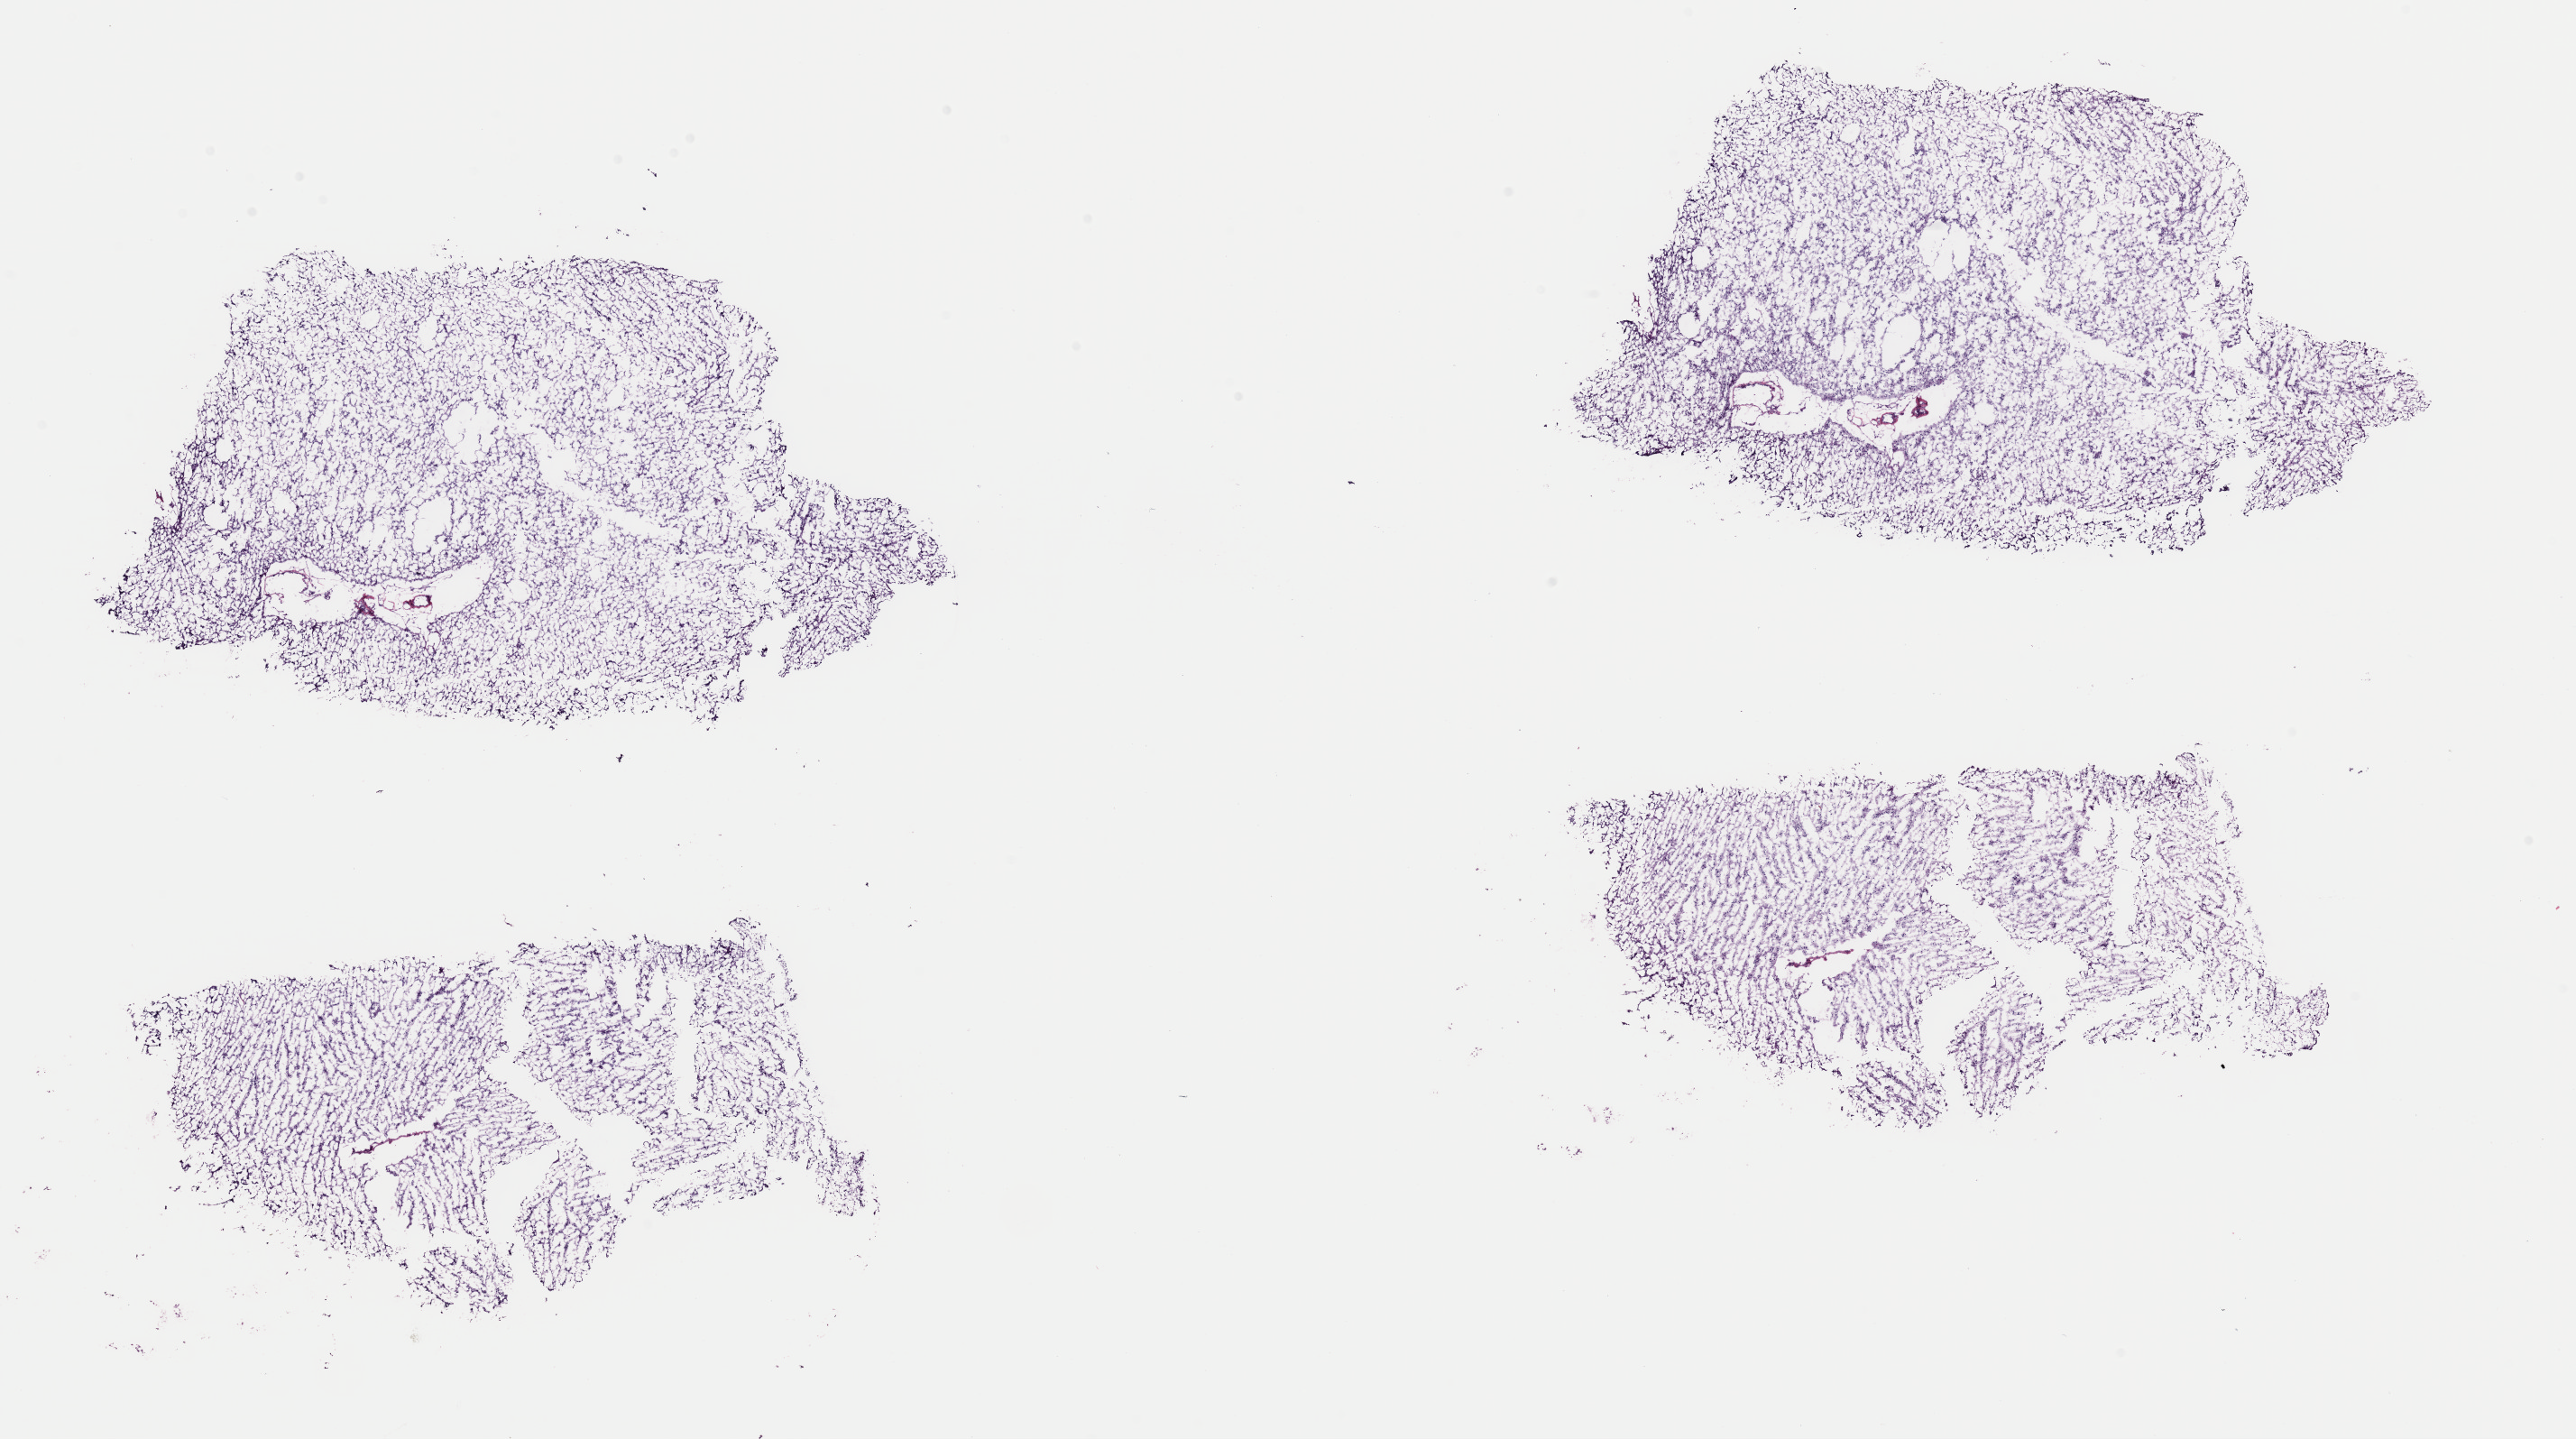
Whole-slide histology image, H&E-stained — whole scanned area (about 22.6 x 12.6 mm, from a 40x scan) shown as a low-resolution overview. Slide review estimates, as recorded: tumour cells 50%, tumour nuclei 80%, normal cells 10%, stromal cells 40%, necrosis 0%. Infiltration values recorded for this section: lymphocyte infiltration 0%, monocyte infiltration 0%, neutrophil infiltration 0%.
* specimen: frozen section from the top of the tissue portion; sample: primary tumour, brain